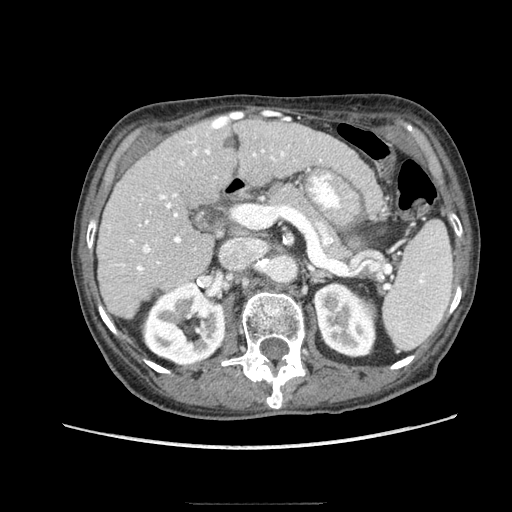
Contrast-enhanced abdominal CT (liver protocol), one axial slice. Position 44 of 83 along the scan axis. Soft-tissue window (W 400 / L 40 HU). 2.5 mm slice thickness. 512 × 512 image matrix, field of view 360 × 360 mm. From the clinical record (not read from this slice): diagnosis: hepatocellular carcinoma (patient treated with transarterial chemoembolisation; whether this scan precedes or follows treatment is not stated here); TNM stage (as recorded): Stage-I; Child-Pugh class: A.
Annotated regions visible in this slice (semi-automatically segmented with operator editing):
- liver parenchyma outside the tumour (the mass and vessels are separate outlines, so this box may not span the whole liver): bounding box <96,114,342,318> (left, top, right, bottom; pixels)
- liver vessels: <117,116,322,271>